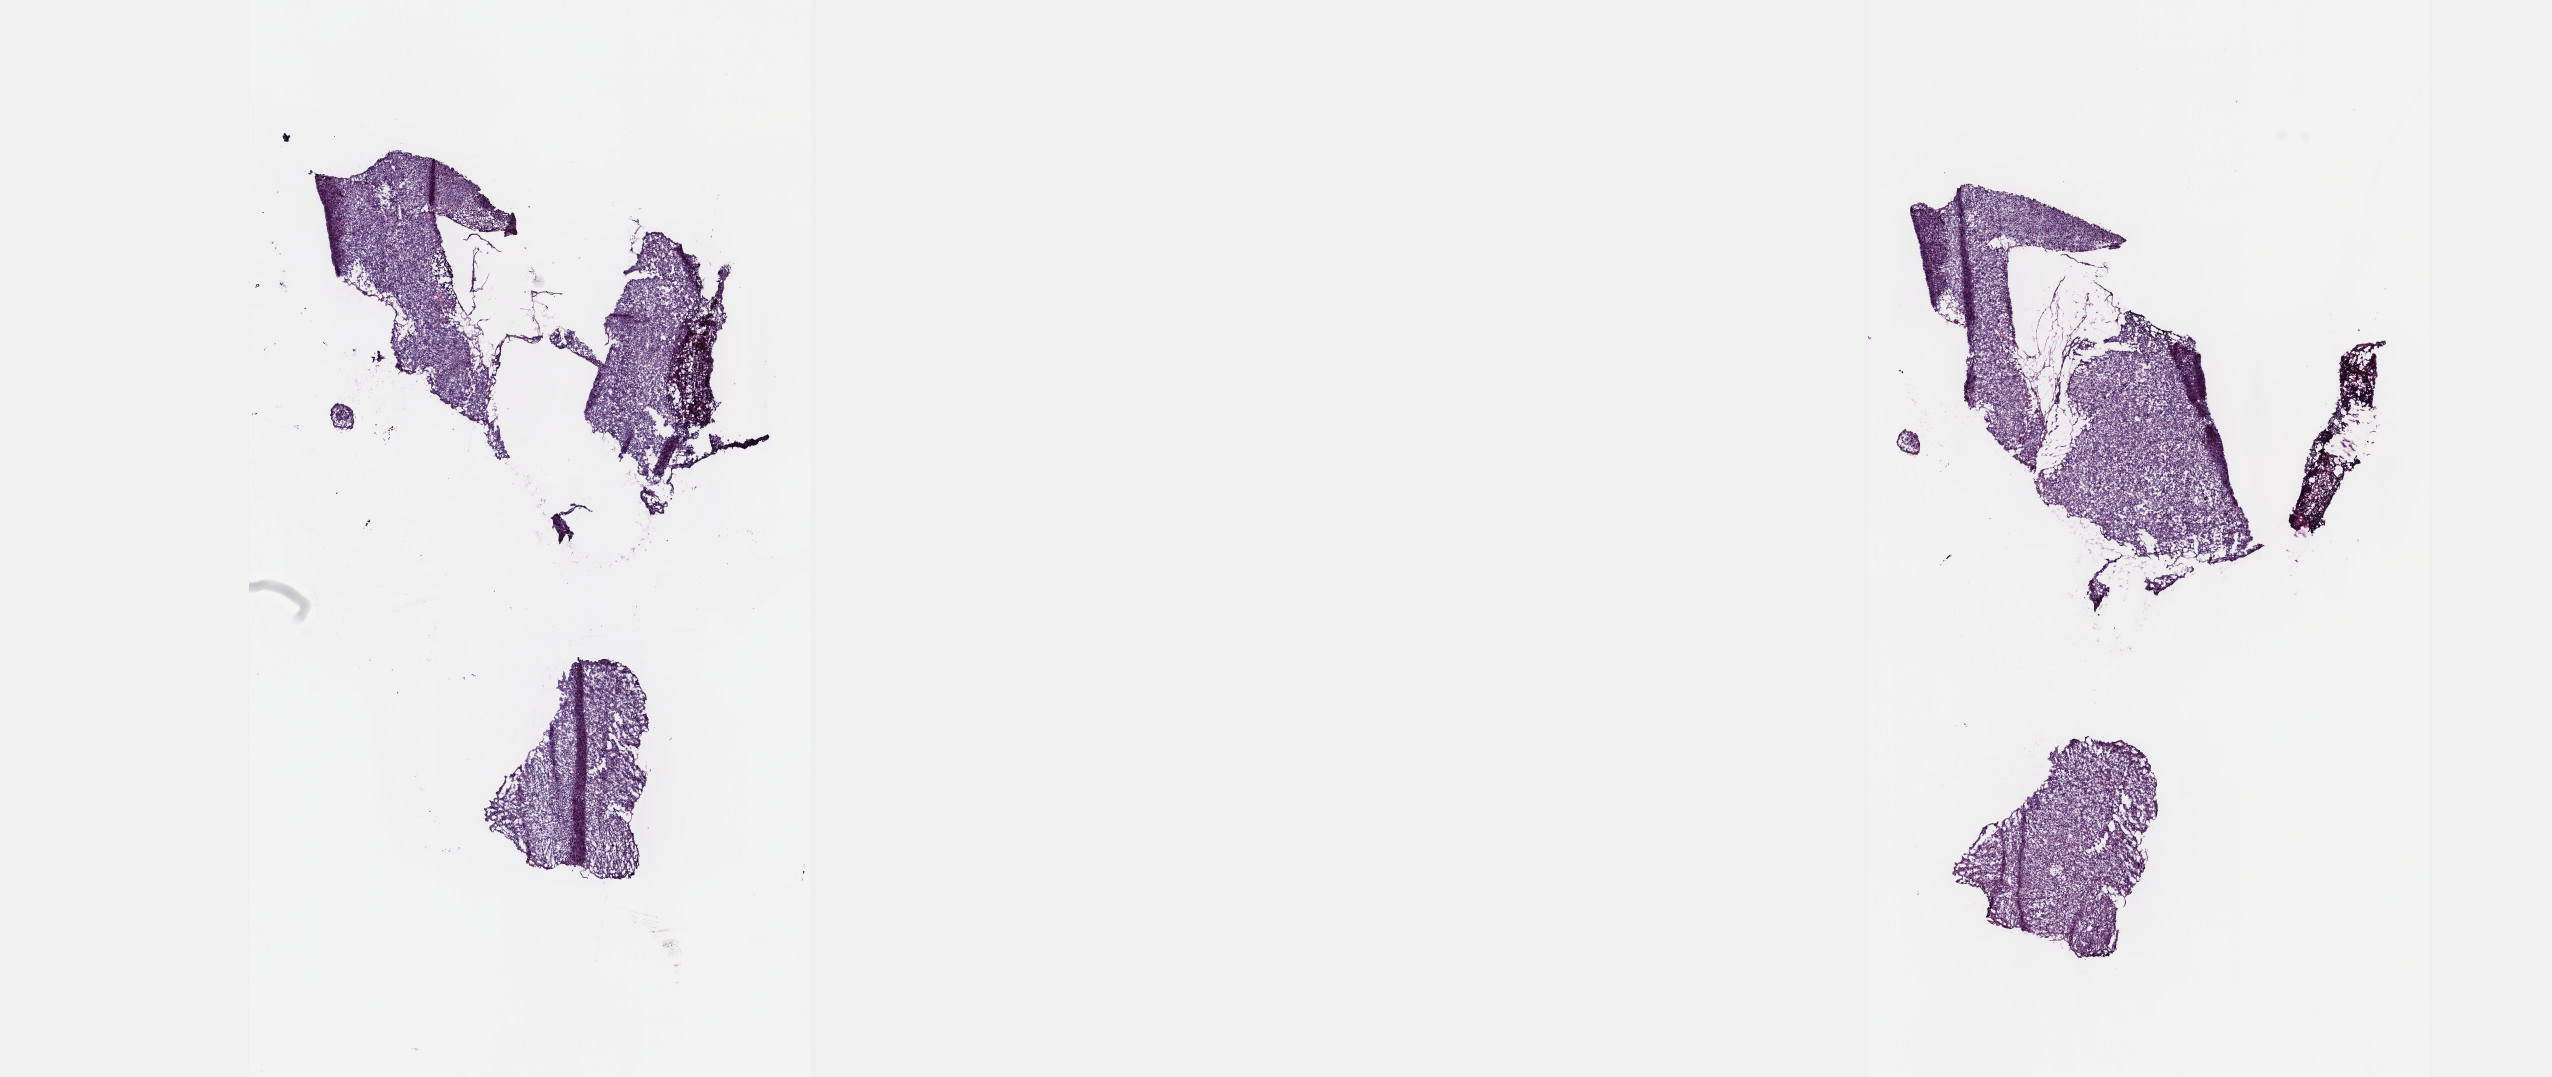
Digitized H&E tissue section (whole slide) — low-resolution overview of the scanned area, about 20.6 x 8.7 mm (acquisition: 40x scan), frozen section, corpus uteri, primary tumour sample. Patient: female, age at initial diagnosis 59 years. Slide review estimates, as recorded: tumour cells 95%, tumour nuclei 100%, normal cells 0%, stromal cells 5%, necrosis 0%. Infiltration values recorded for this section: lymphocyte infiltration 0%, monocyte infiltration 0%, neutrophil infiltration 0%.
Histologic diagnosis: Leiomyosarcoma, NOS (myometrium).